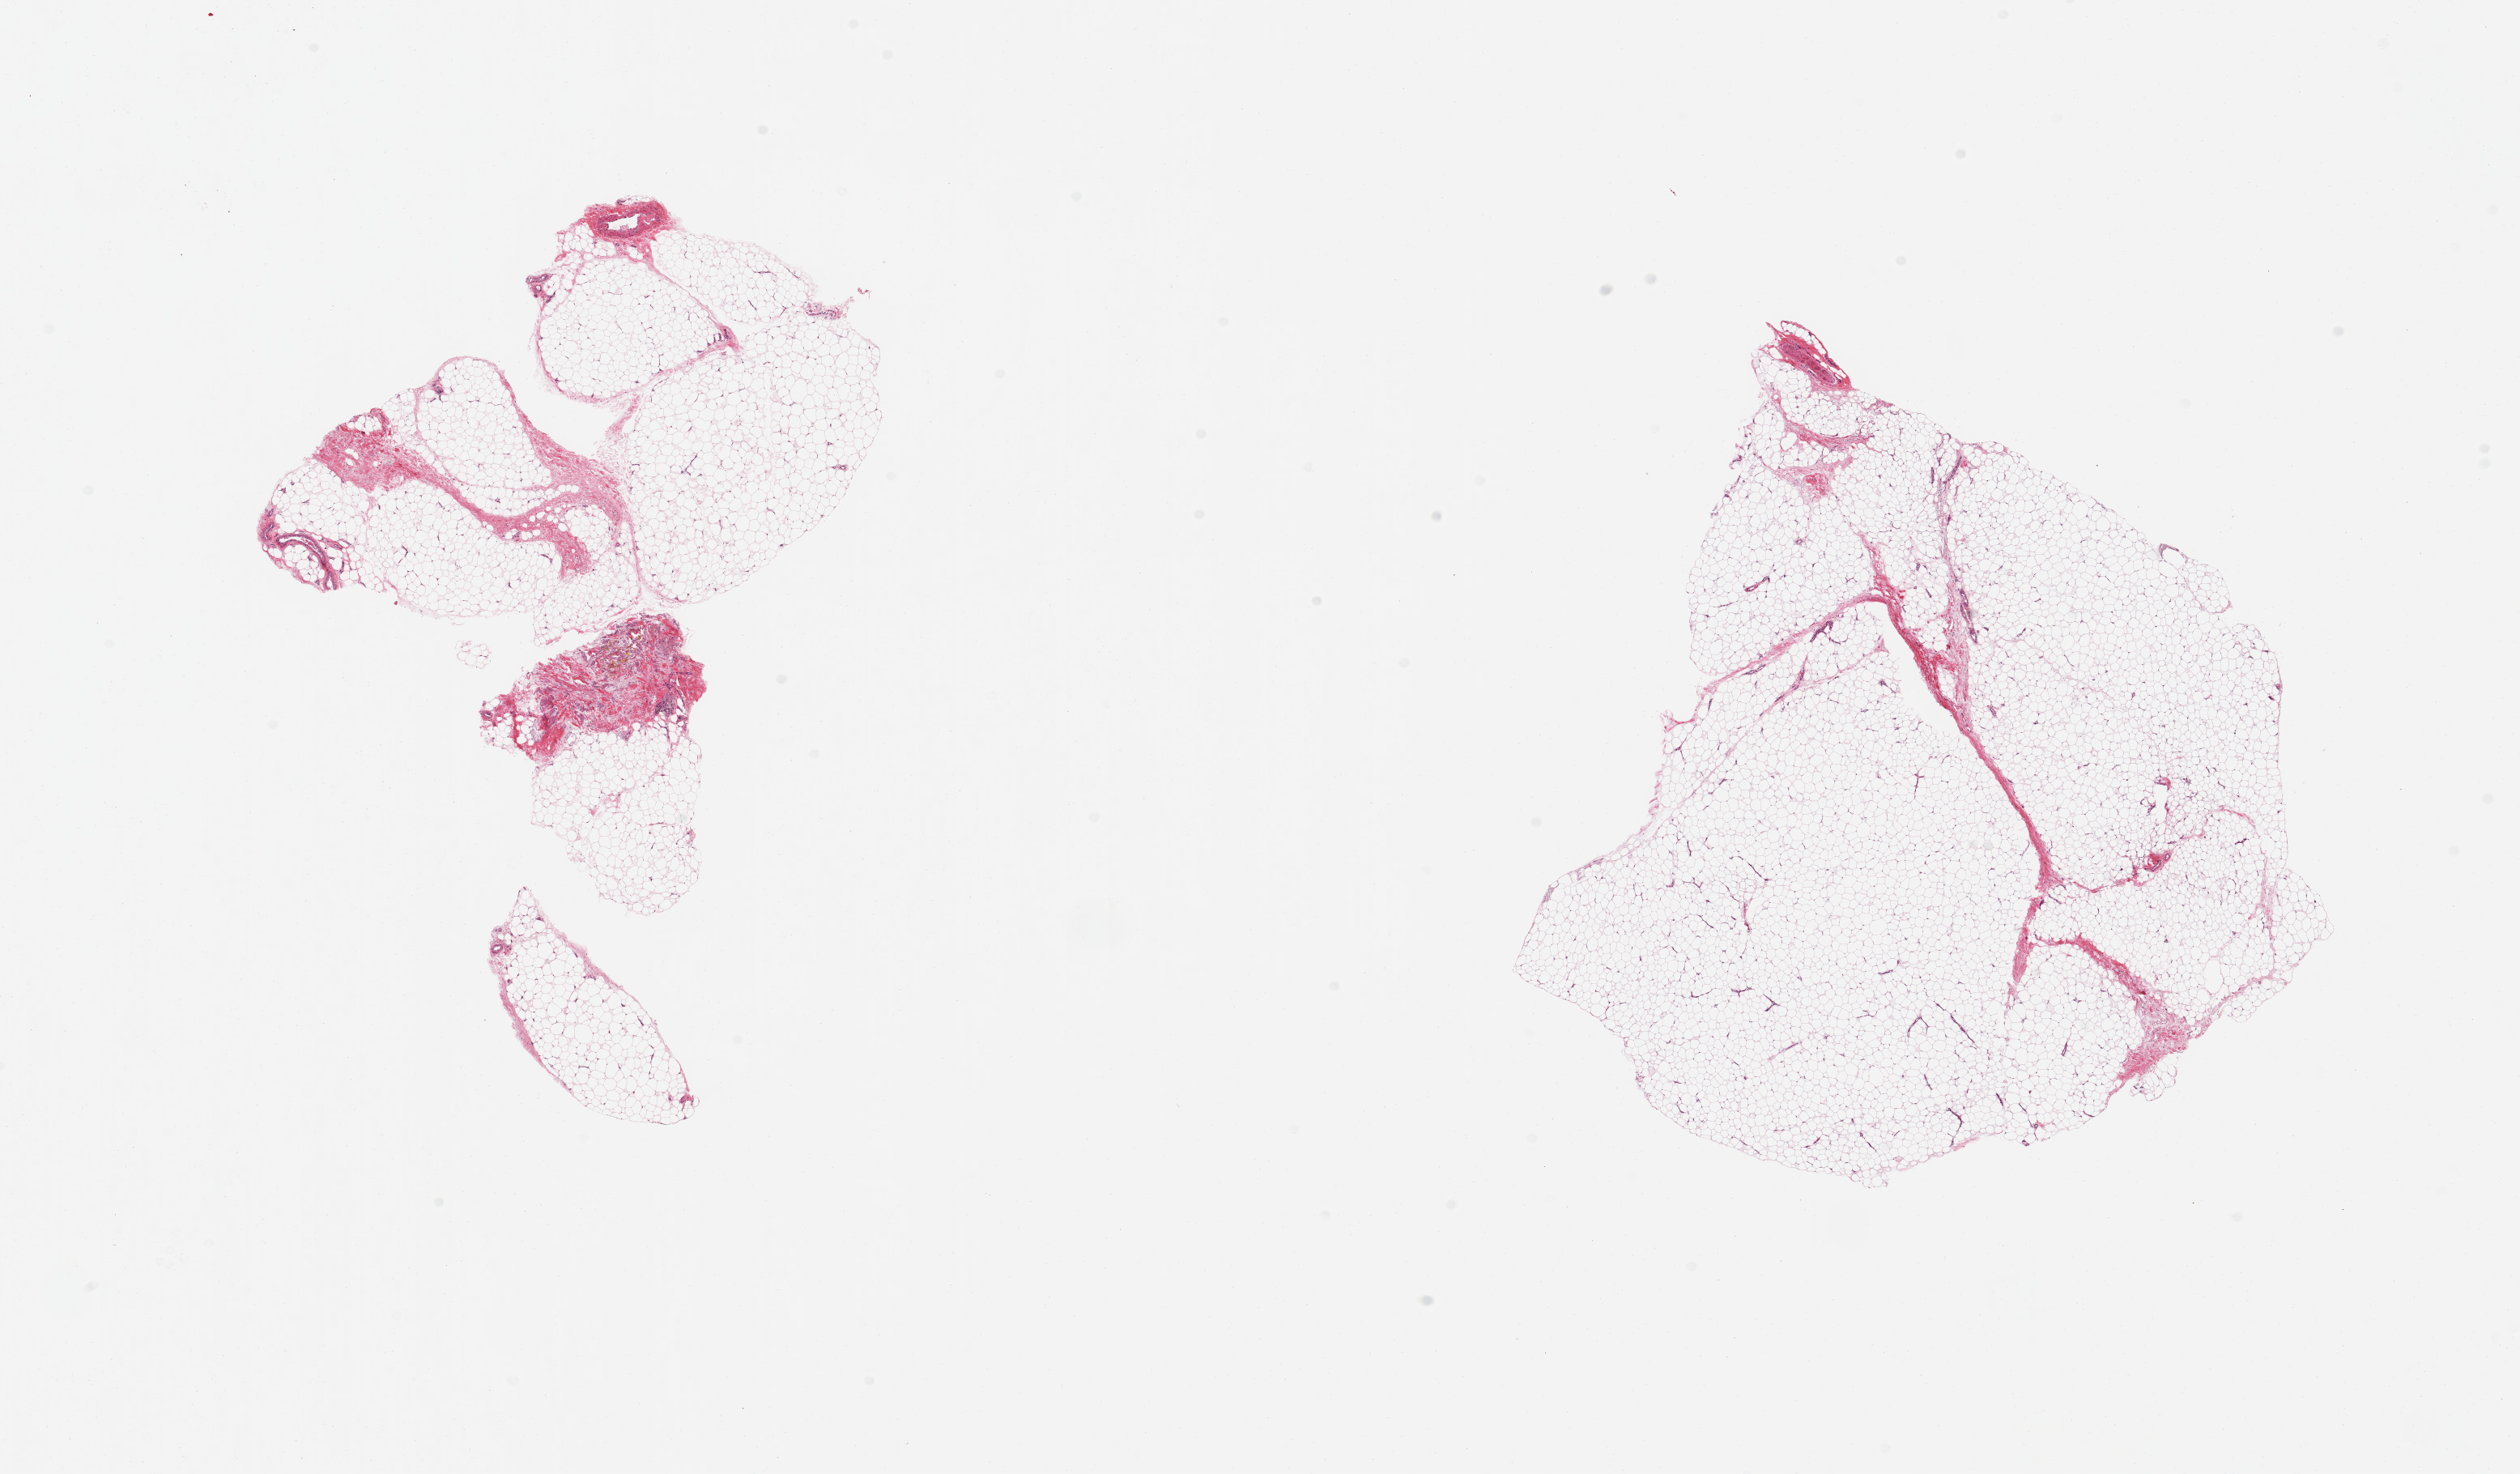
H&E whole-slide image — shown as a low-resolution overview of the whole scanned area (about 24.6 x 14.4 mm, slide scanned at 20x). PAXgene-fixed, paraffin-embedded tissue. Sampled site (target tissue): adipose tissue. Donor tissue sample.
- pathologist's review note for this sample: 2 pieces, ~15% fascia/vascular elements